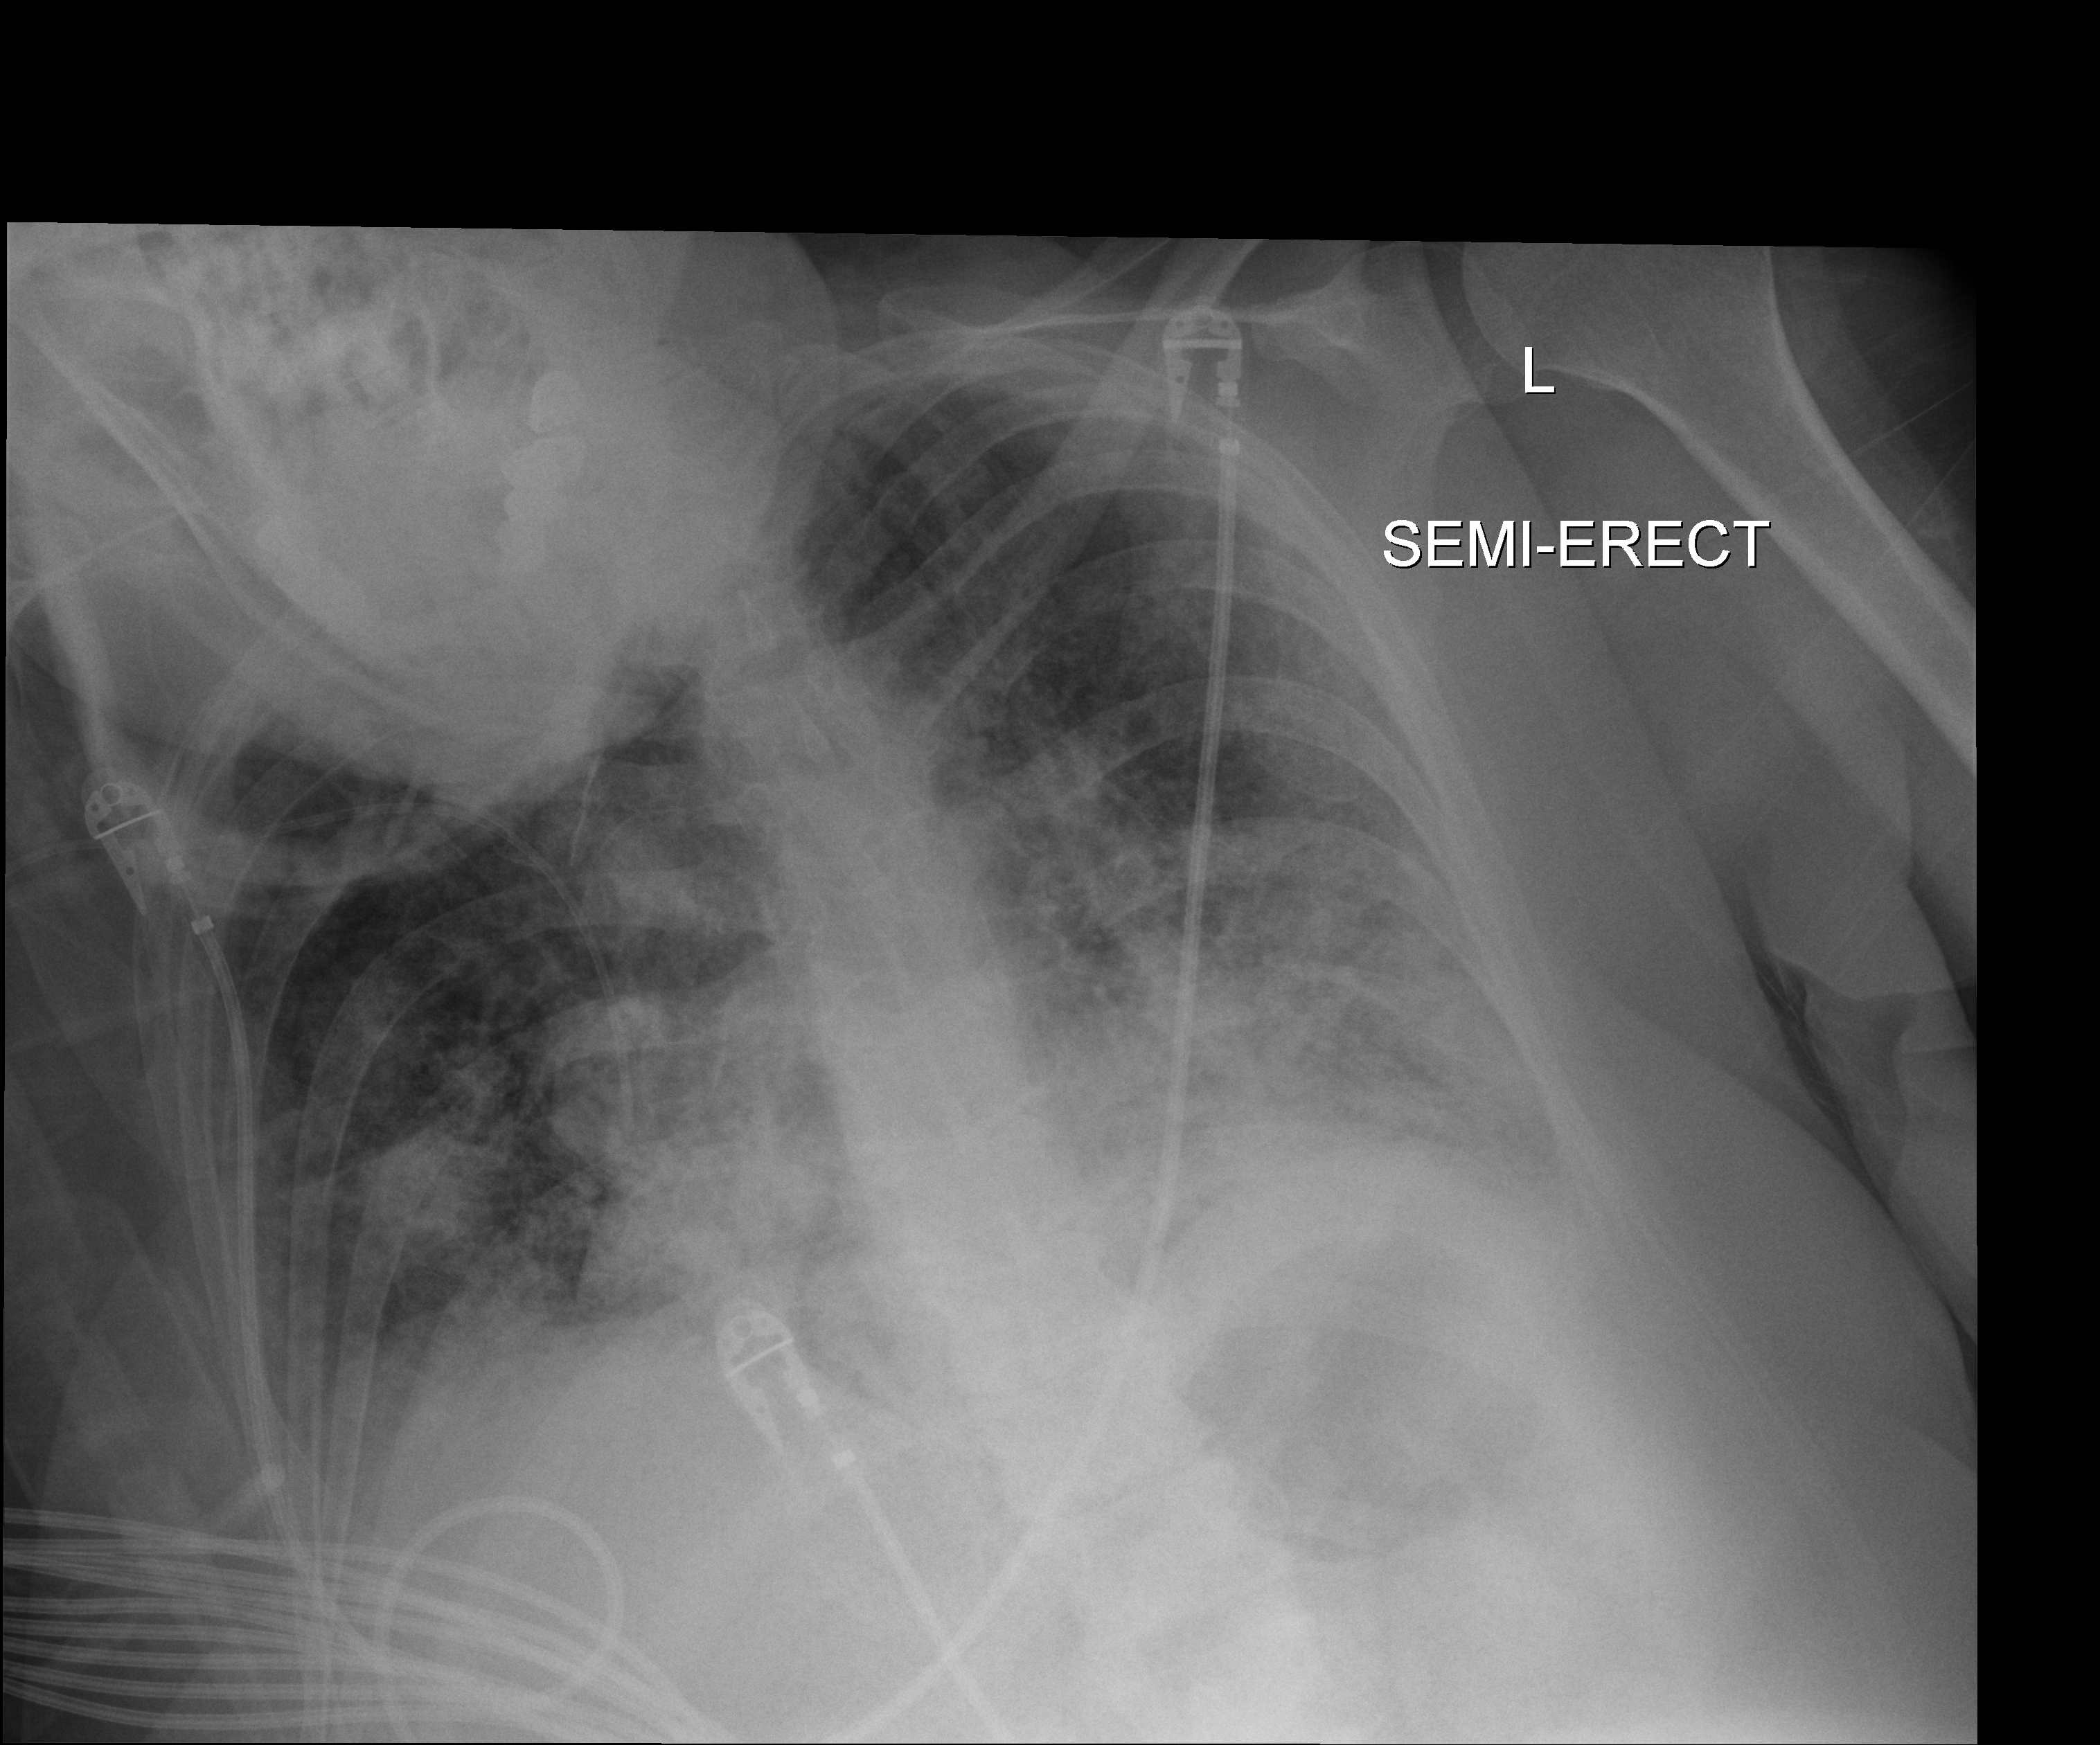
Bedside chest radiograph (digital radiography), anteroposterior (AP) projection. Patient hospitalised with COVID-19; female, aged 60–74 years.
Admission-level facts for this patient (not findings on this image; timing relative to this image not recorded): smoking status (admission record): never; mechanically ventilated during this hospital stay: yes; admitted to intensive care during this hospital stay: yes.